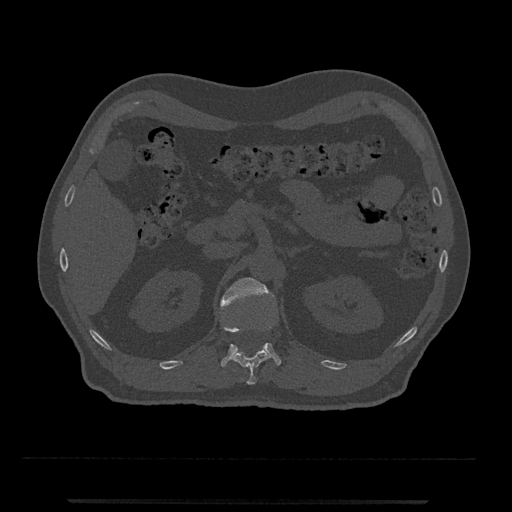
CT including the spine, one axial slice. Position 370 of 797 along the scan axis. Reconstruction kernel Br40s/3. 120 kVp. Bone window (W 1800 / L 400 HU). 512 × 512 image matrix. Male patient, age 63 years. Case-level facts recorded for this patient, not image findings: primary cancer: prostate.
Annotated regions visible in this slice (semi-automatic segmentation, software-assisted and operator-edited):
- L1 vertebra: bounding box [x1, y1, x2, y2] px = [220, 277, 281, 367]
- T12 vertebra: [222, 308, 270, 385]